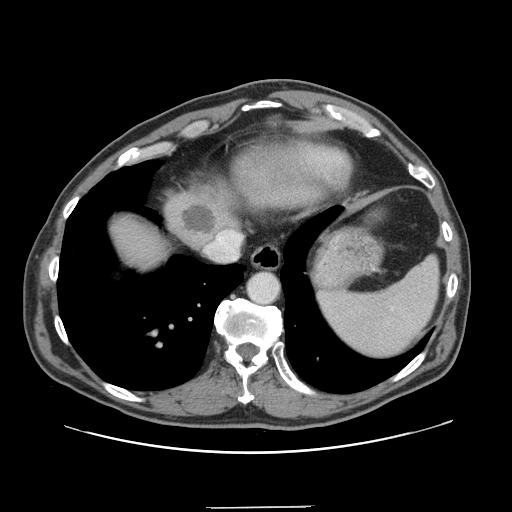
Contrast-enhanced abdominal CT, one axial slice. Slice 128 of 139 in the series (ordered by position). Intravenous contrast given. Soft-tissue window (W 400 / L 40 HU). 2.5 mm slice thickness. 512 × 512 image matrix, field of view 397 × 397 mm. Male patient, age 64 years. Case-level facts recorded for this patient, not image findings: diagnosis: colorectal cancer liver metastases, imaged before liver resection; multiple liver metastases: yes; largest metastasis: 3.5 cm; disease in both lobes: yes.
Outlined on this slice (manually delineated by an expert):
- liver: bounding box (x1, y1, x2, y2) in pixels: (113, 188, 237, 267)
- planned liver remnant (the part of the liver to remain after resection): (113, 188, 237, 265)
- liver metastasis: (183, 207, 215, 235)